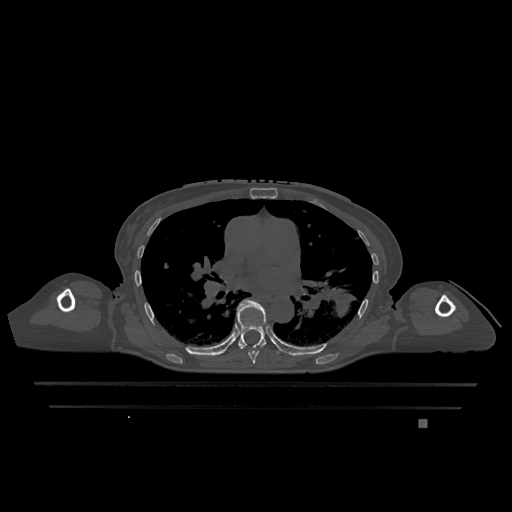
CT including the spine, one axial slice; position 762 of 1317 along the scan axis; bone window (W 1800 / L 400 HU); 0.5 mm slice thickness; 512 × 512 image matrix. Female patient, age 74 years. Case-level facts recorded for this patient, not image findings: primary cancer: lung.
Outlined on this slice (semi-automatically segmented with operator editing):
- T6 vertebra: bounding box [x1, y1, x2, y2] px = [240, 327, 267, 364]
- T7 vertebra: [237, 299, 279, 354]